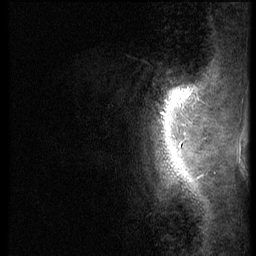
Breast MRI (dynamic contrast-enhanced), one sagittal slice; slice 6 of 56 in the series (ordered by position); 3 images stored at this slice position (order not interpretable as contrast timing); 1.5 T; TE 4.2 ms, TR 9 ms; 2.5 mm slice thickness; 256 × 256 image matrix, field of view 180 × 180 mm. Patient: female, 46 years. From the clinical record (not read from this slice): setting: breast cancer imaged before/during neoadjuvant chemotherapy; receptor status: HER2-positive.
Structures marked on this image (semi-automatic segmentation, software-assisted and operator-edited):
- analysis volume of interest (the breast-tissue region the enhancement analysis was run in; not a lesion): box from (x=132, y=68) to (x=190, y=143) px
- tumour enhancement mask (voxels above the 140 % enhancement threshold inside the analysis volume of interest): (x=180, y=93)–(x=190, y=98)